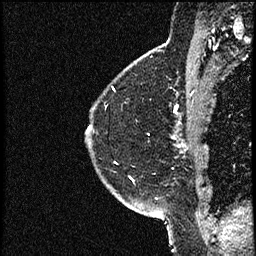
Breast MRI (dynamic contrast-enhanced), one sagittal slice; slice 43 of 52 in the series (ordered by position); dynamic contrast-enhanced study with each time point stored as its own series, time point 2 of 3 at this slice position (early post-contrast, ordered by acquisition time); 1.5 T; TE 4.2 ms, TR 17.6 ms; 2 mm slice thickness; 256 × 256 image matrix, field of view 200 × 200 mm. Female patient, age 49 years. Case-level facts recorded for this patient, not image findings: setting: breast cancer imaged before/during neoadjuvant chemotherapy; receptor status: HER2-positive.
Outlined on this slice (semi-automatically segmented with operator editing):
- analysis volume of interest (the breast-tissue region the enhancement analysis was run in; not a lesion): bounding box [x1, y1, x2, y2] px = [86, 65, 182, 175]
- tumour enhancement mask (voxels above the 100 % enhancement threshold inside the analysis volume of interest): [176, 105, 179, 108]